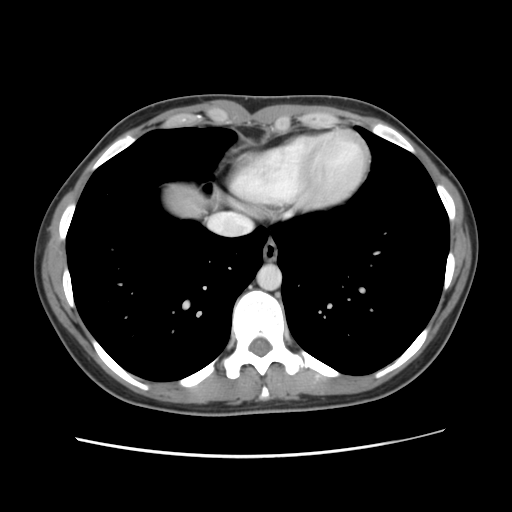
Contrast-enhanced abdominal CT, one axial slice; position 120 of 134 along the scan axis; intravenous contrast given; soft-tissue window (W 400 / L 40 HU); 2.5 mm slice thickness; 512 × 512 image matrix, field of view 339 × 339 mm. Female patient, age 33 years. From the clinical record (not read from this slice): diagnosis: colorectal cancer liver metastases, imaged before liver resection; multiple liver metastases: yes; largest metastasis: 4.5 cm.
Annotated regions visible in this slice (manually delineated by an expert):
- liver: bounding box [x1, y1, x2, y2] px = [163, 183, 210, 218]
- planned liver remnant (the part of the liver to remain after resection): [165, 182, 211, 218]